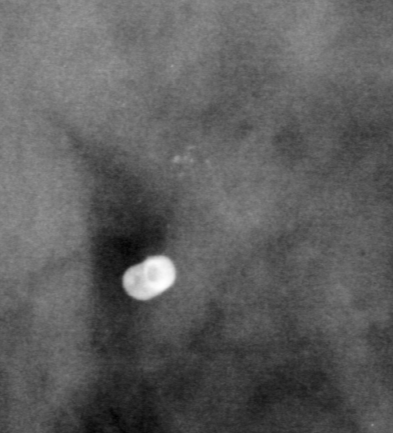
Crop from a digitized film mammogram around one marked abnormality; left breast; CC view; BI-RADS breast density category 4 (scale 1–4).
Marked abnormality: calcifications, morphology amorphous, distribution clustered; BI-RADS assessment category 4; pathology (as recorded): benign.